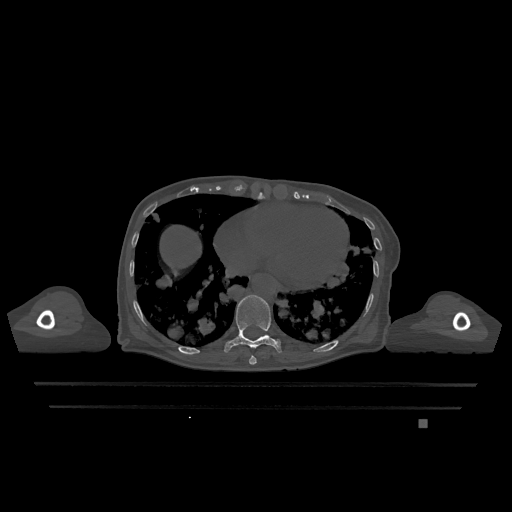
CT including the spine, one axial slice. Position 644 of 1317 along the scan axis. Bone window (W 1800 / L 400 HU). 0.5 mm slice thickness. 512 × 512 image matrix, field of view 500 × 500 mm. Patient: female, 74 years. From the clinical record (not read from this slice): primary cancer: lung; vertebrae with lytic lesions (as recorded): T1, T4, T5, T6, L4, L5.
Outlined on this slice (semi-automatically segmented with operator editing):
- T10 vertebra: bounding box [x1, y1, x2, y2] px = [224, 295, 282, 353]
- T9 vertebra: [249, 355, 257, 365]